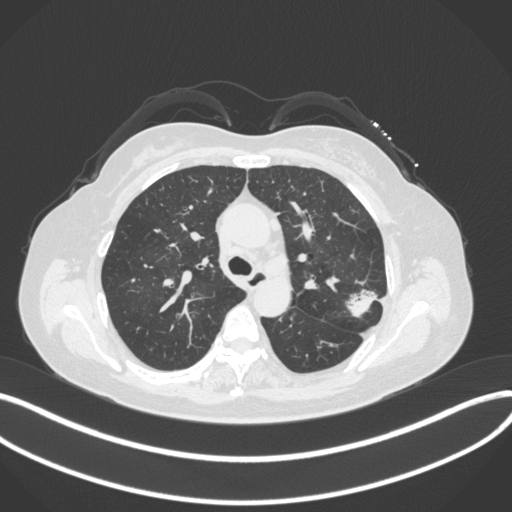
Chest CT, one axial slice; position 232 of 330 along the scan axis; reconstruction kernel B31f; 120 kVp; lung window (W 1500 / L -600 HU); 1 mm slice thickness; 512 × 512 image matrix, field of view 400 × 400 mm. Female patient, age 60 years. From the clinical record (not read from this slice): clinical TNM (as recorded): T1c N0 M0.
Outlined on this slice (bounding box drawn by a radiologist):
- lung tumour (recorded histology: adenocarcinoma): bounding box (x1, y1, x2, y2) in pixels: (342, 285, 380, 321)